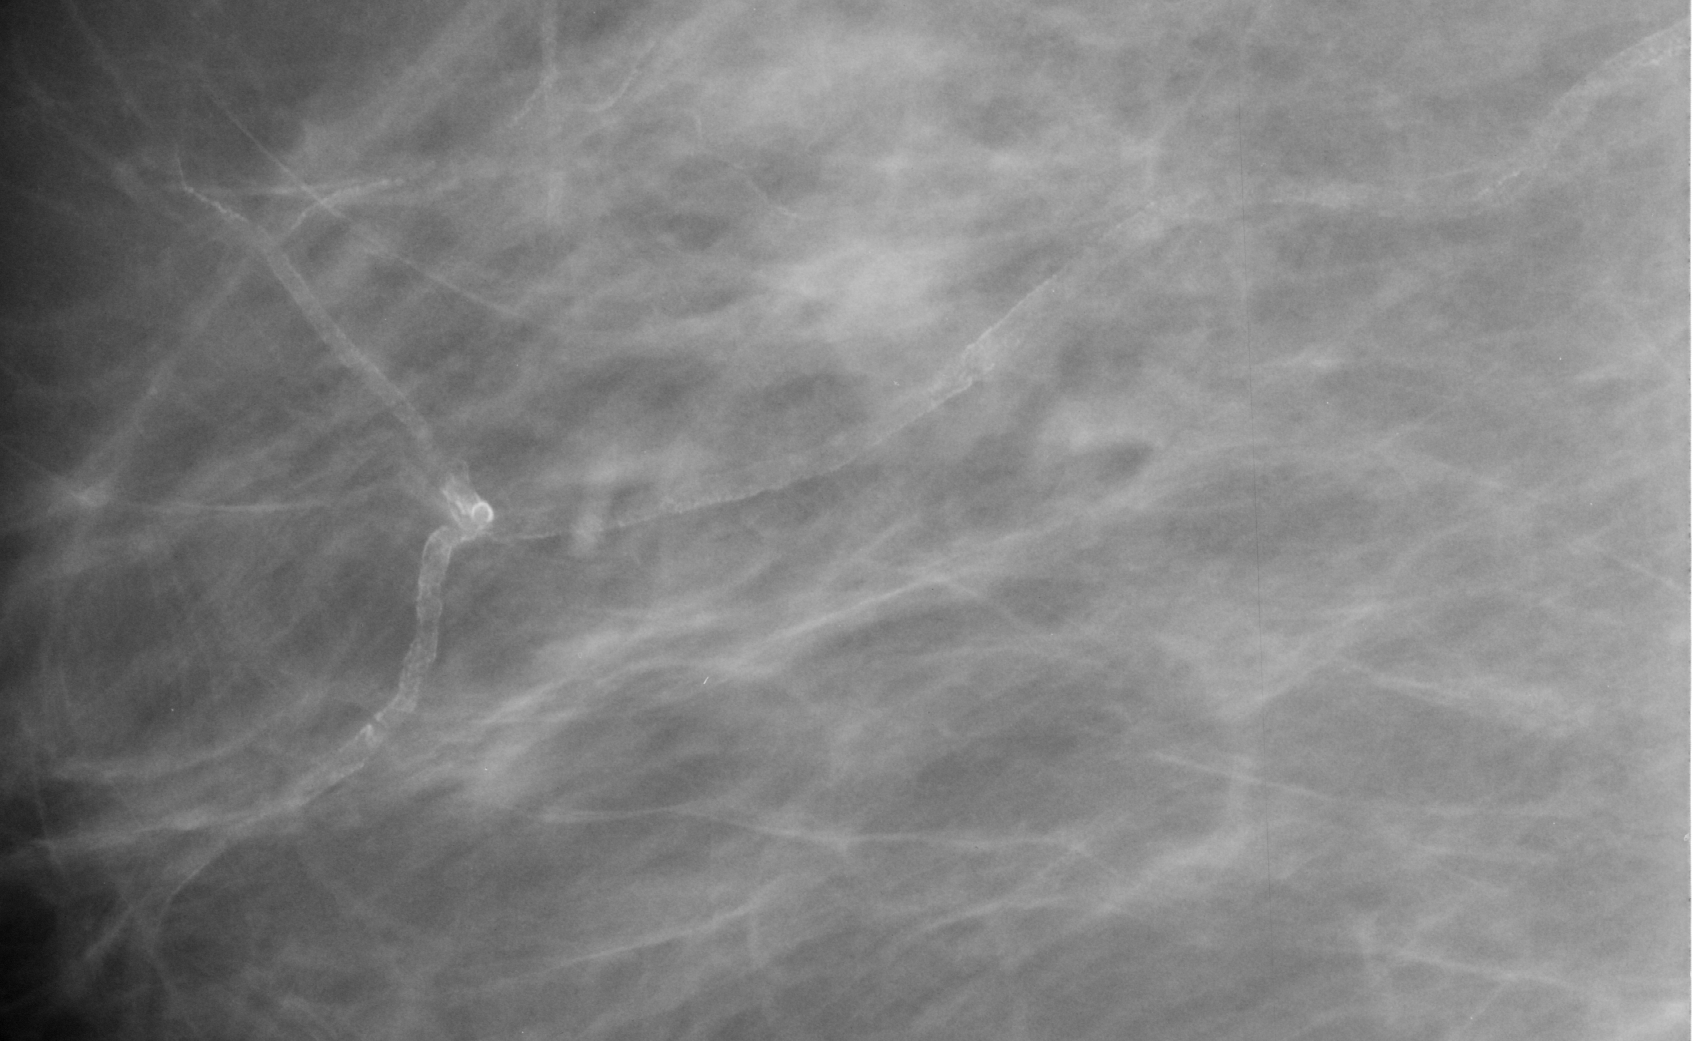
Crop from a digitized film mammogram around one marked abnormality; right breast; MLO view.
Marked abnormality: calcifications, morphology vascular; BI-RADS assessment category 2; benign; no additional work-up was recommended (benign without callback).